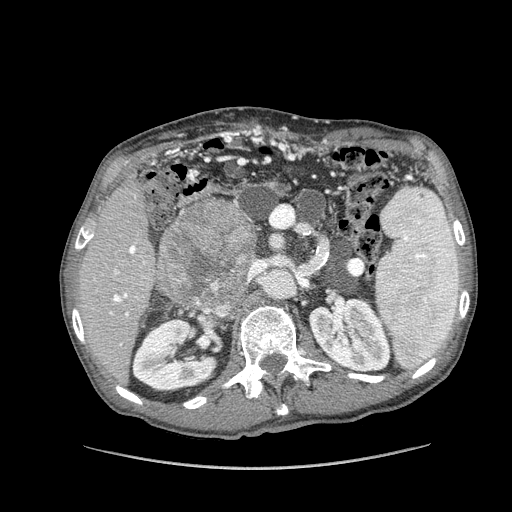
Contrast-enhanced abdominal CT (liver protocol), one axial slice. Slice 59 of 162 in the series (ordered by position). Reconstruction kernel STANDARD. 100 kVp. Soft-tissue window (W 400 / L 40 HU). 2.5 mm slice thickness. 512 × 512 image matrix, field of view 400 × 400 mm. Case-level facts recorded for this patient, not image findings: diagnosis: hepatocellular carcinoma (patient treated with transarterial chemoembolisation; whether this scan precedes or follows treatment is not stated here); TNM stage (as recorded): Stage-IIIA; Child-Pugh class: A; tumour nodularity: multinodular; tumour size: 9.9 cm.
Outlined on this slice (semi-automatically segmented with operator editing):
- liver parenchyma outside the tumour (the mass and vessels are separate outlines, so this box may not span the whole liver): bounding box <78,178,156,380> (left, top, right, bottom; pixels)
- mass: <158,201,258,305>
- liver vessels: <110,246,145,345>